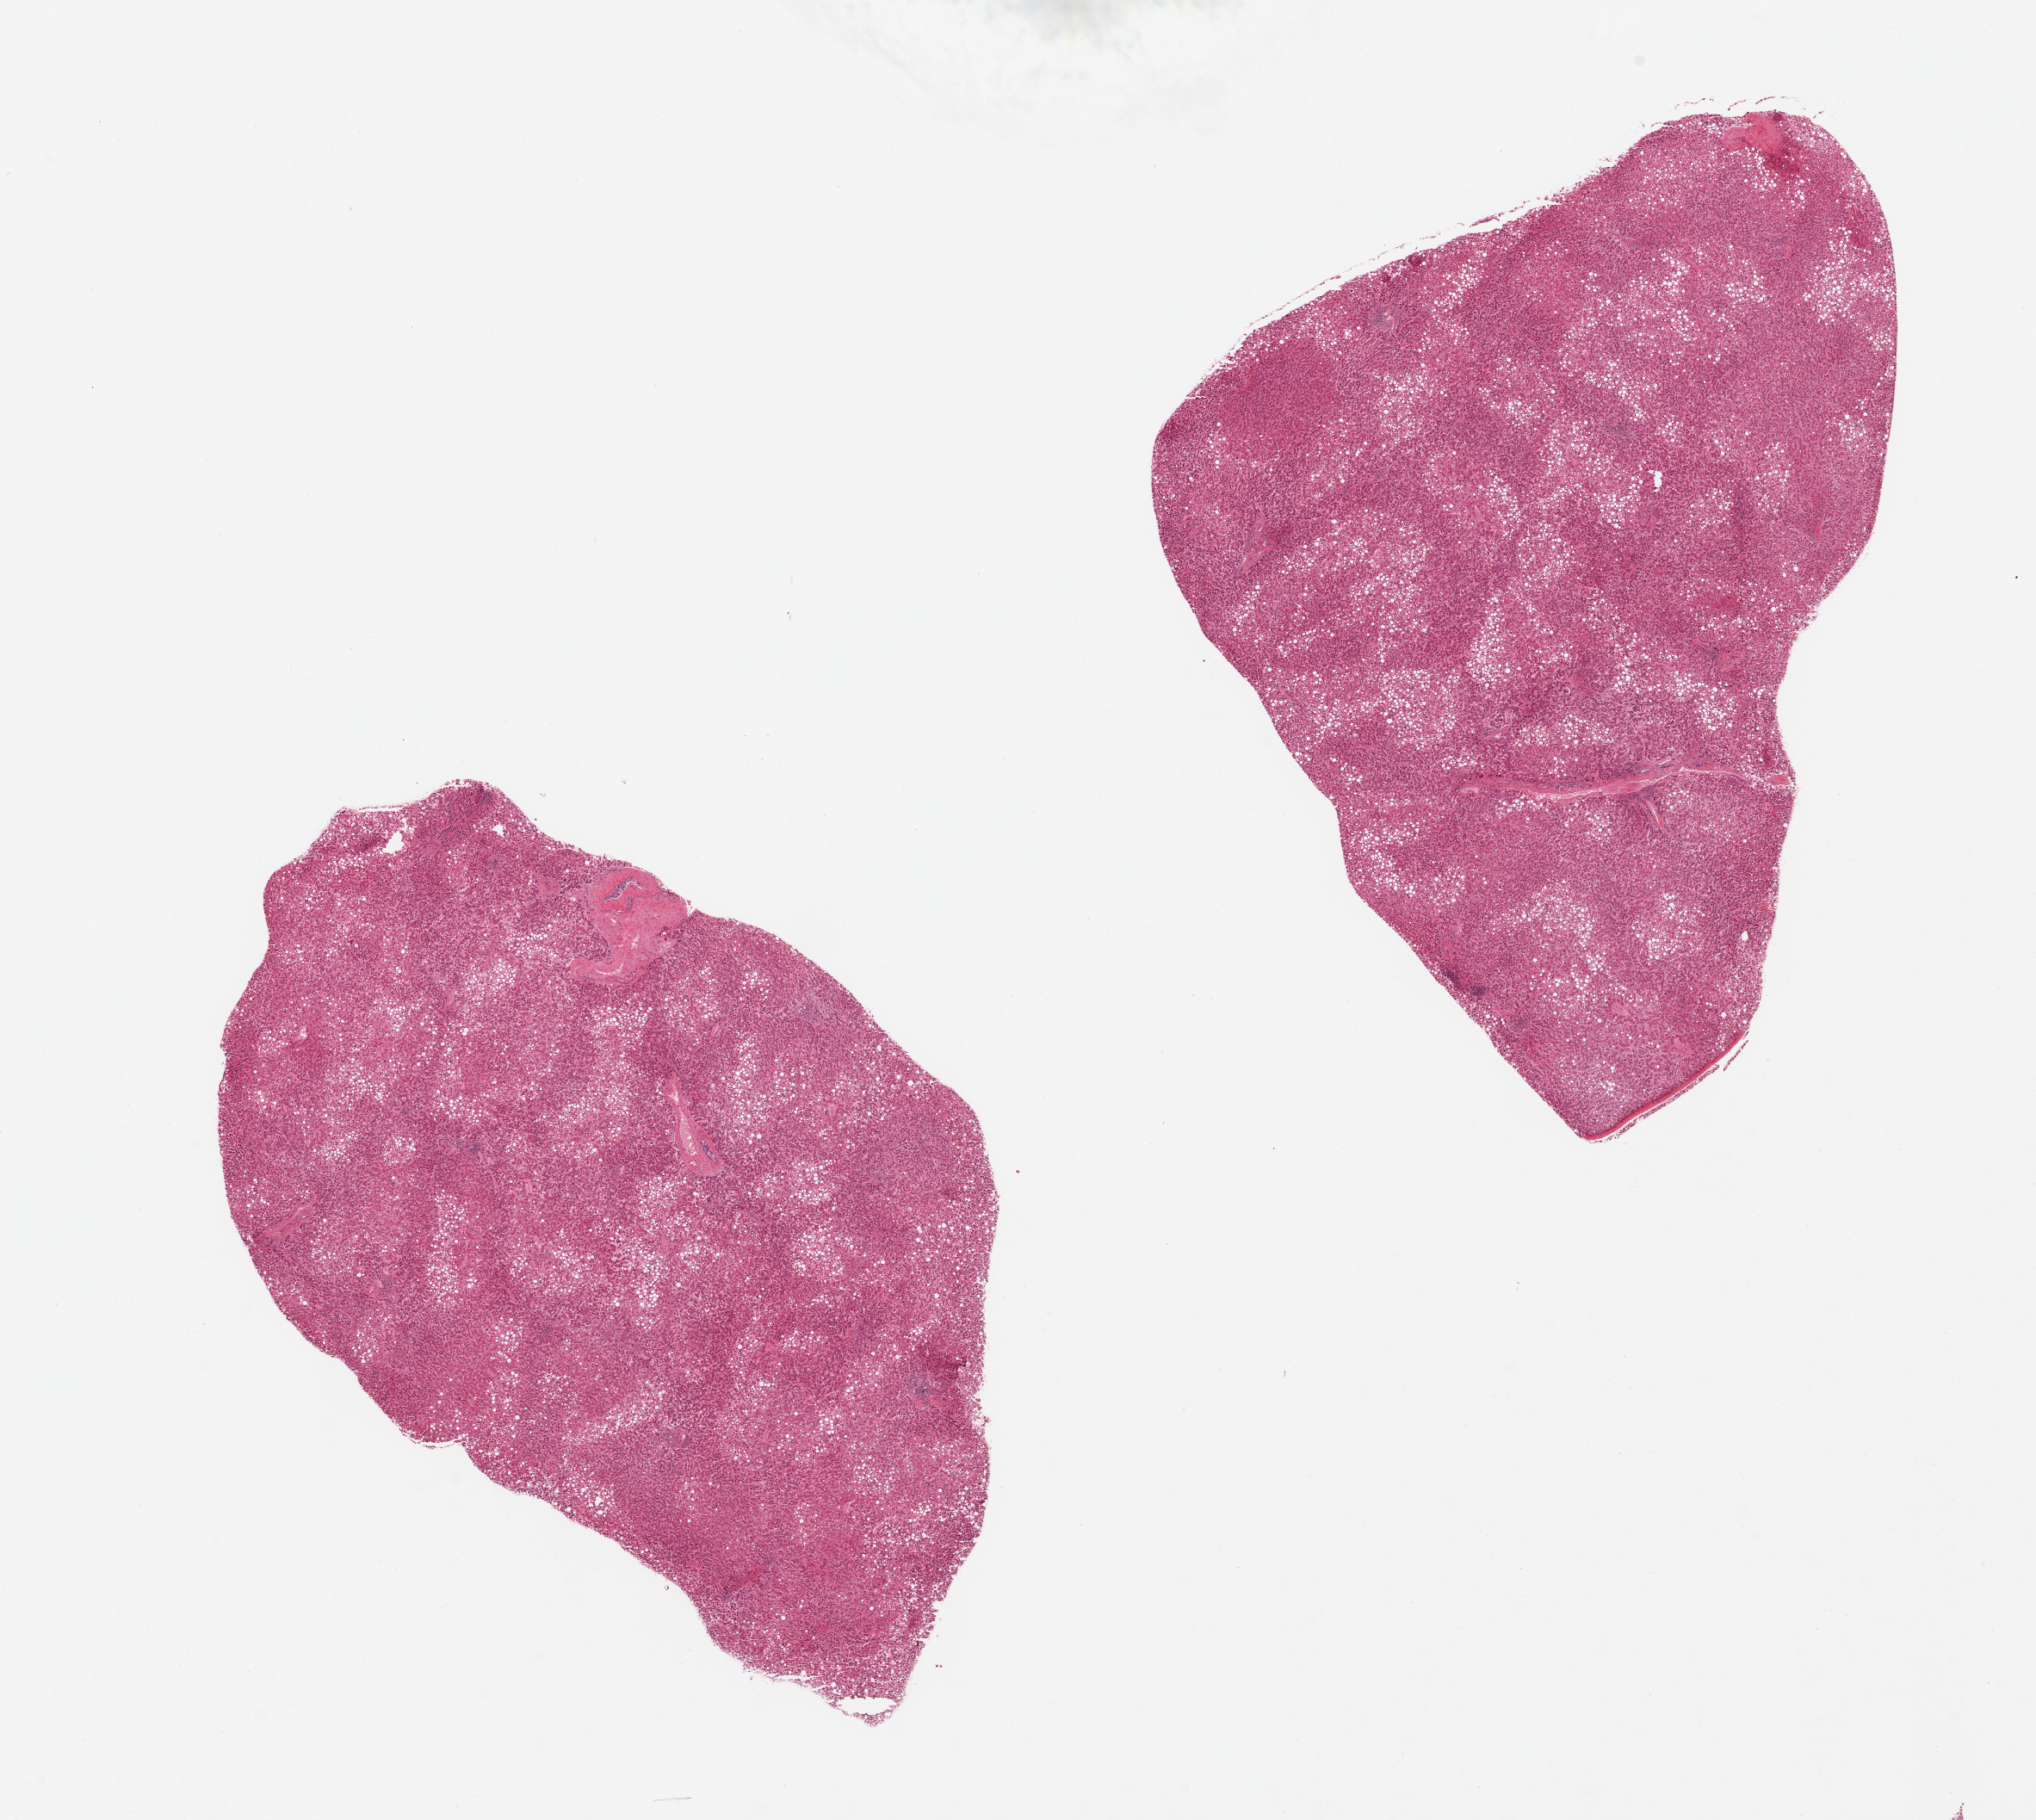
Digitized hematoxylin and eosin (H&E)-stained section, brightfield — whole scanned area (about 18.7 x 16.7 mm) shown as a low-resolution overview, PAXgene-fixed, paraffin-embedded tissue, sampled site (target tissue): liver, donor tissue sample. Donor sex: female.
Pathologist's review note for this sample: 2 pieces. Diffuse macrovesicular steatosis, moderately autolyzed.